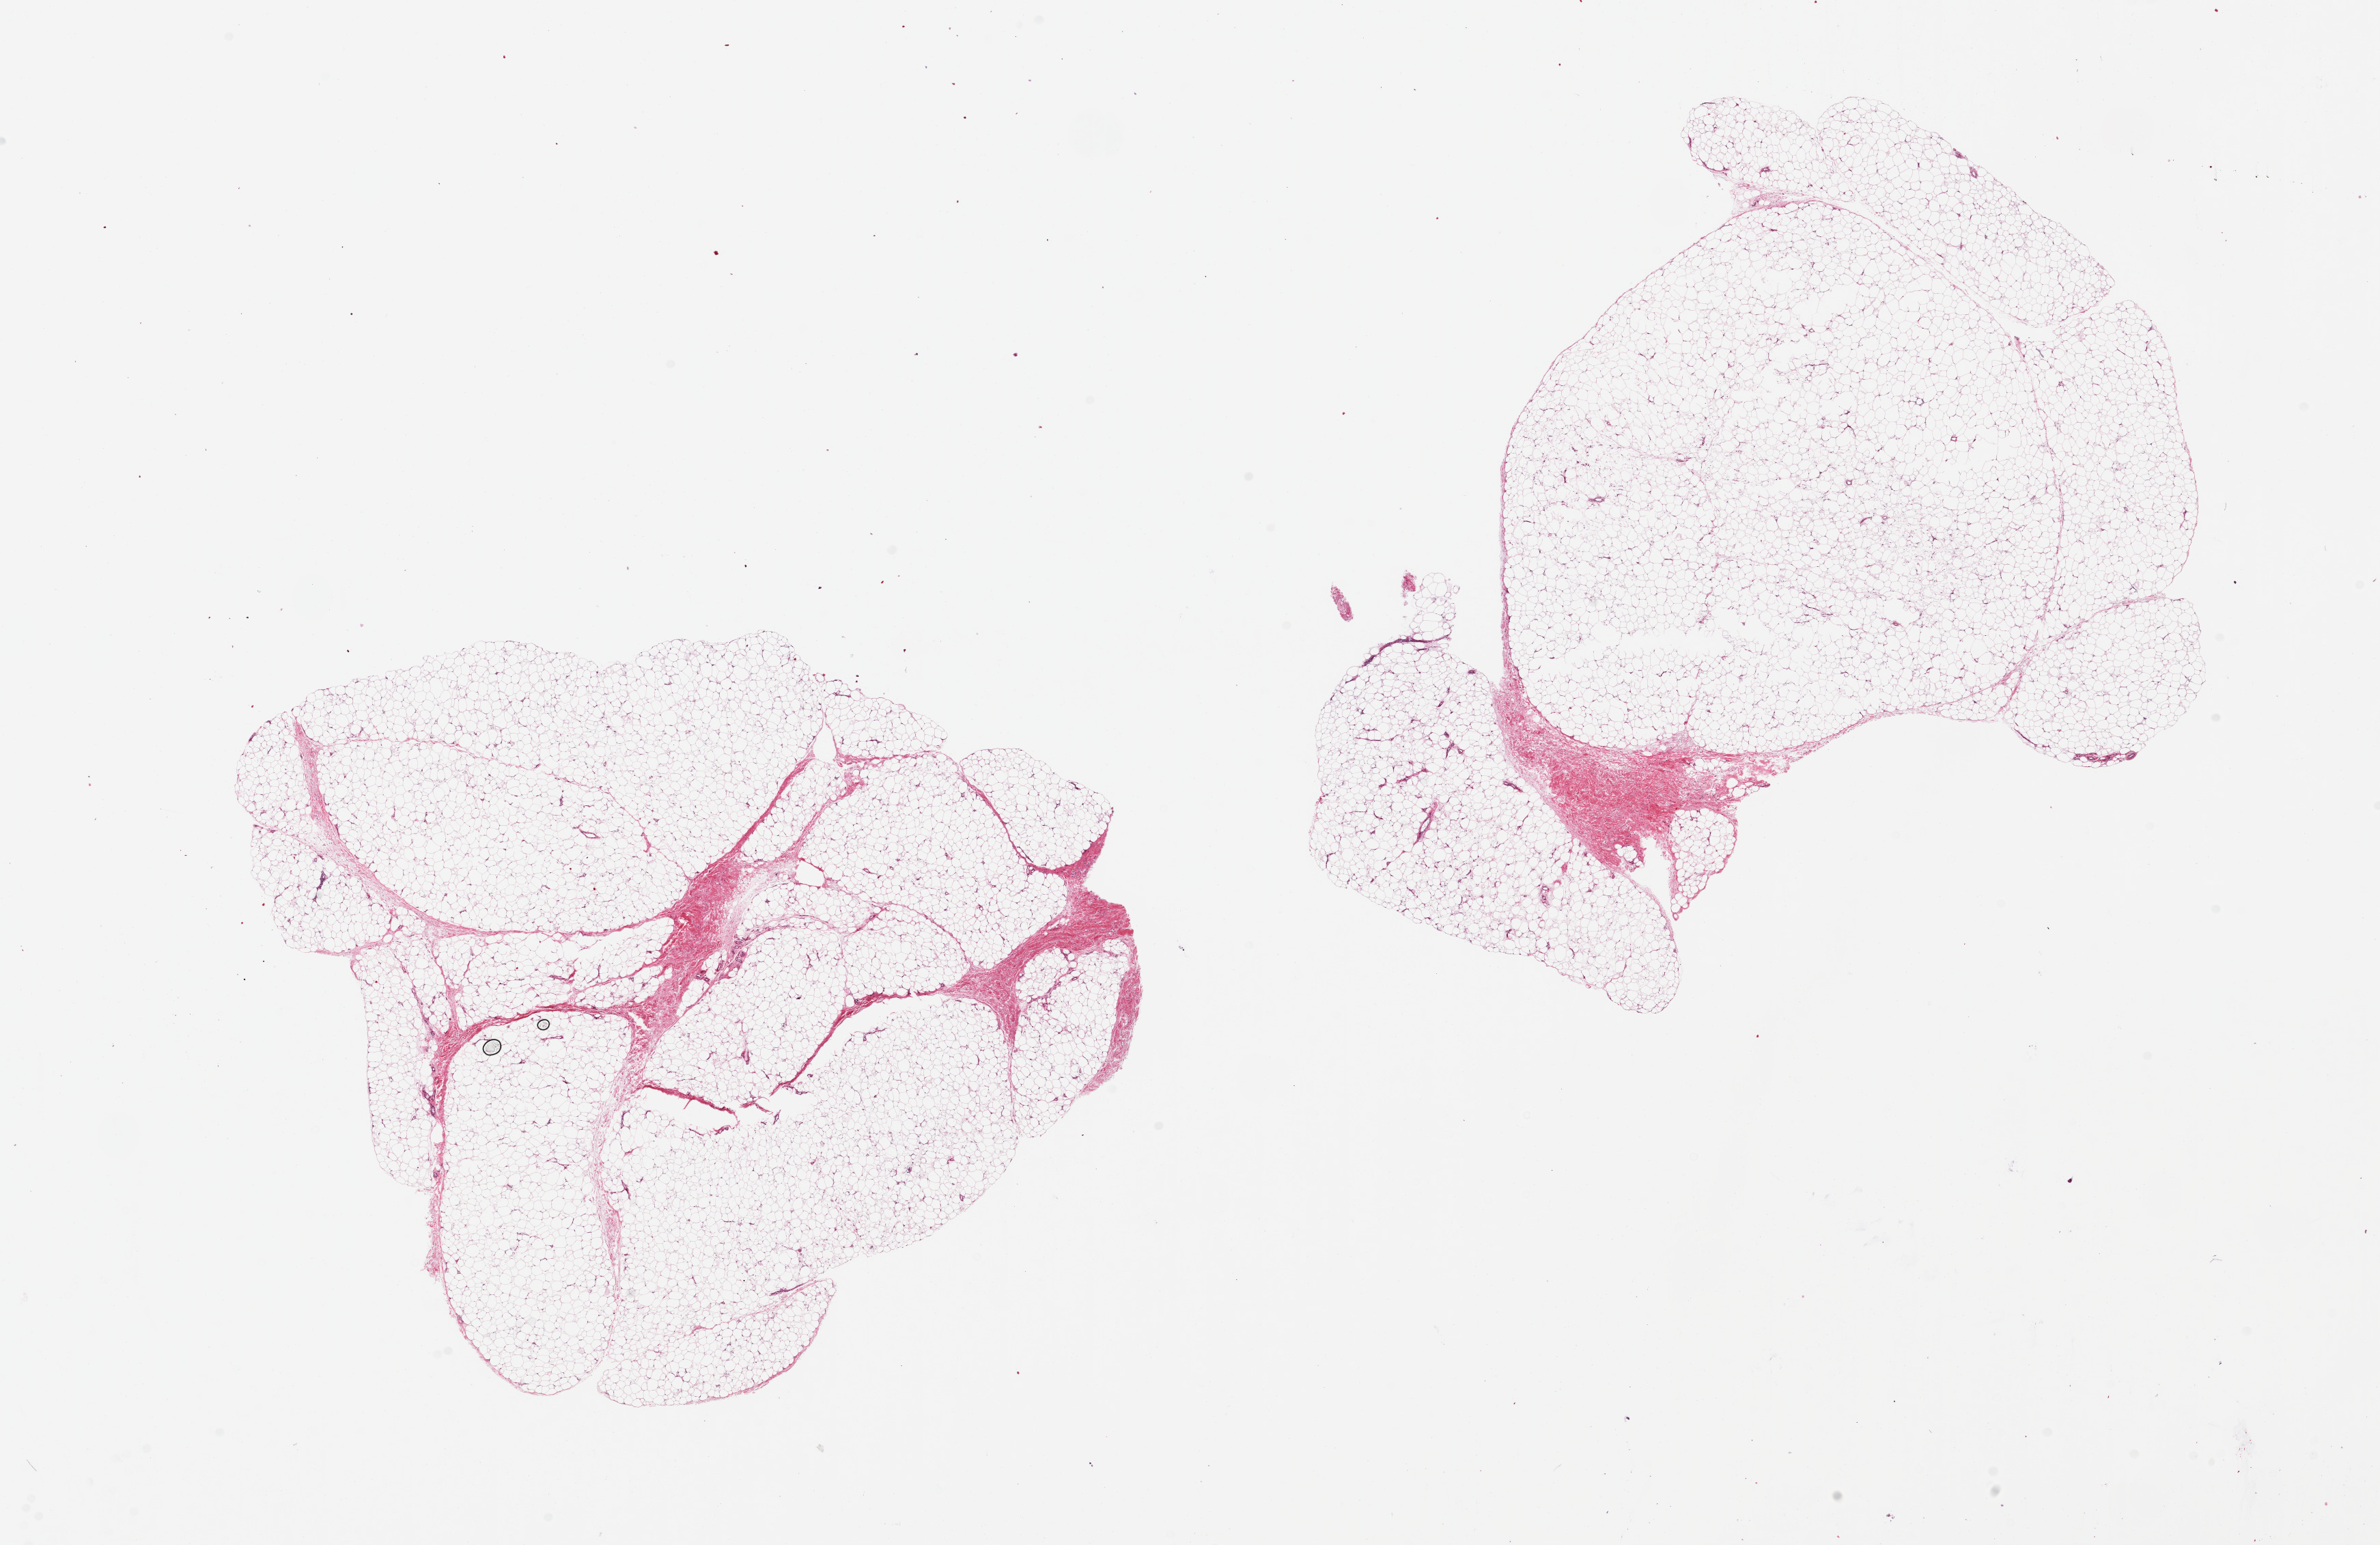
Digitized haematoxylin and eosin-stained section, shown as a low-resolution overview of the whole scanned area (about 27.6 x 17.9 mm), PAXgene-fixed paraffin-embedded (PFPE) section, target tissue: adipose tissue, tissue donor sample. Donor: male.
Pathologist's review note for this sample: 2 pieces ~11x9mm.